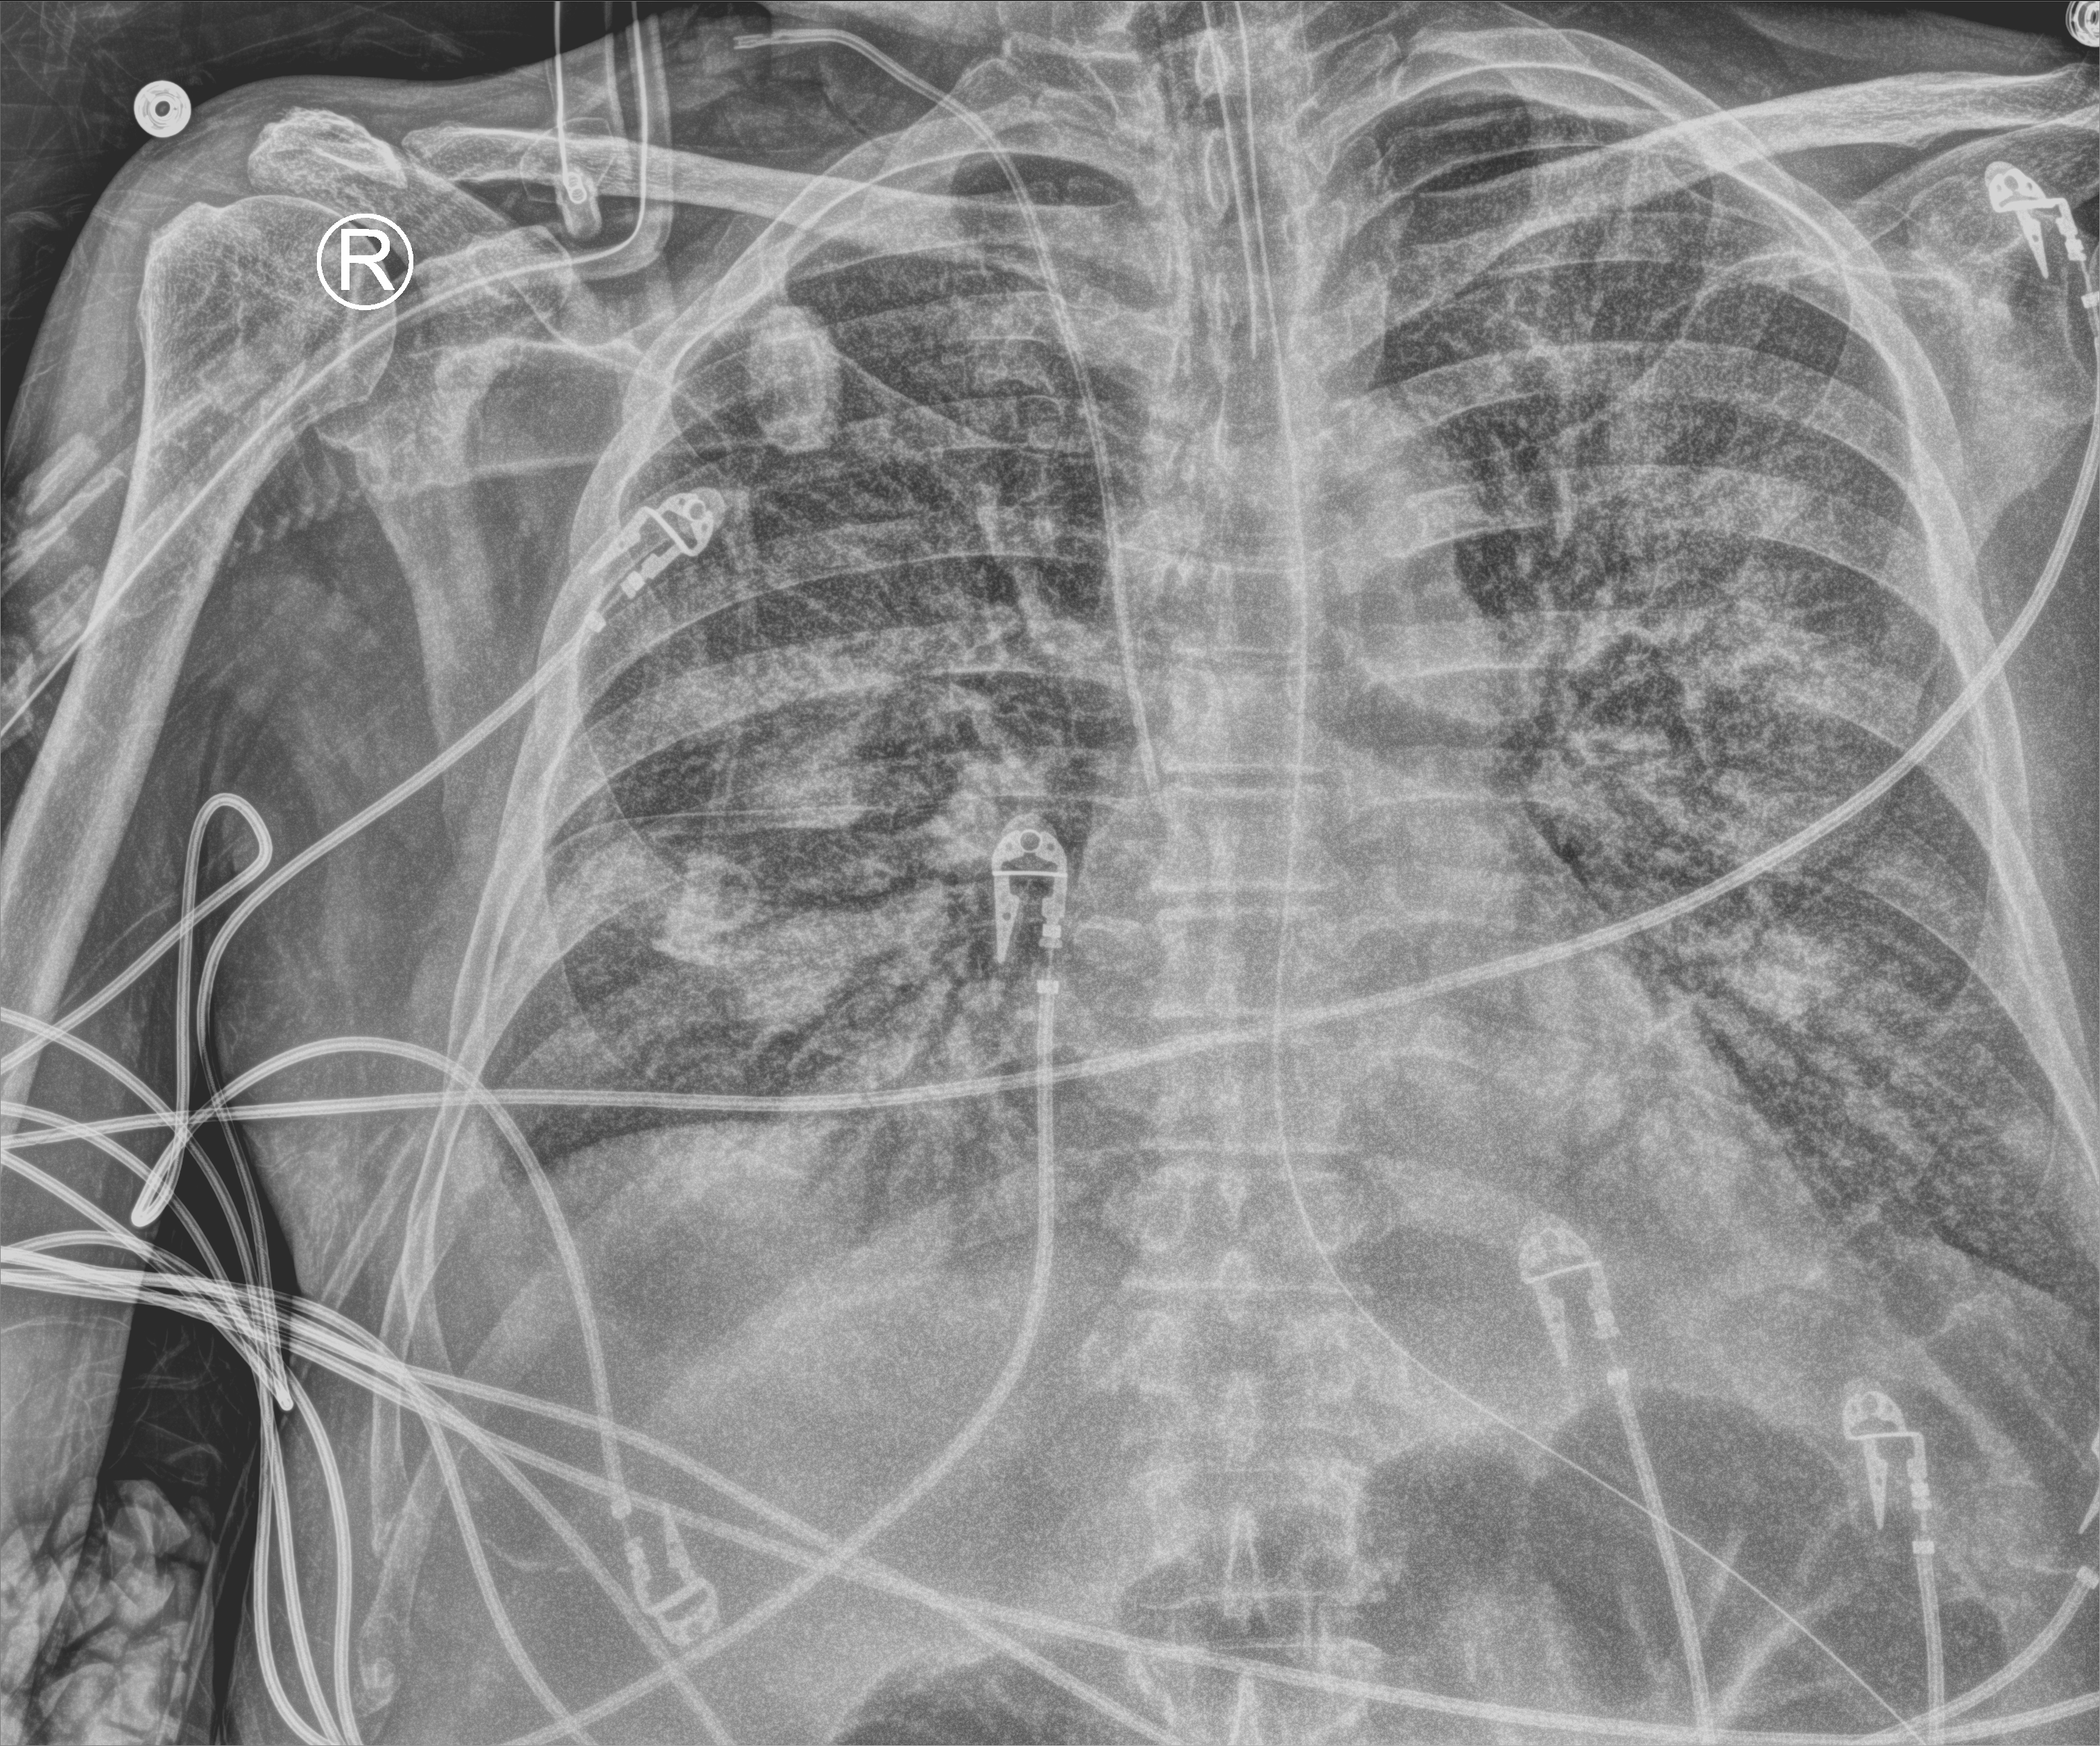
Chest X-ray (portable), anteroposterior (AP) projection. Patient hospitalised with COVID-19; male, aged 60–74 years.
Admission-level facts for this patient (not findings on this image; timing relative to this image not recorded): diabetes (admission record): yes; length of hospital stay: 24 days; admitted to intensive care during this hospital stay: yes.